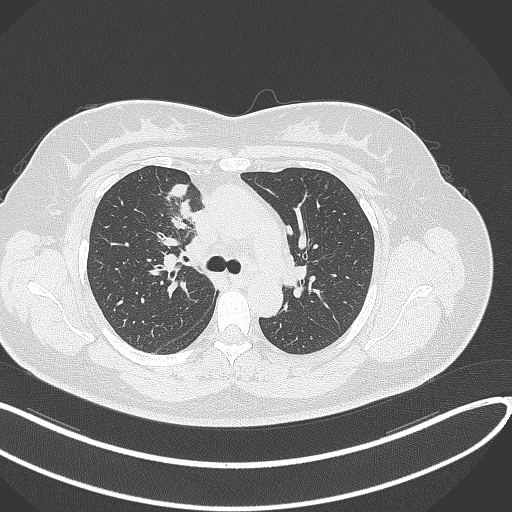
Chest CT, one axial slice; slice 188 of 303 in the series (ordered by position); reconstruction kernel B70f; 120 kVp; lung window (W 1500 / L -600 HU); 1 mm slice thickness; 512 × 512 image matrix. Female patient, age 46 years. Case-level facts recorded for this patient, not image findings: clinical TNM (as recorded): T2a N1 M0.
Outlined on this slice (rectangle marked by the reading radiologist):
- lung tumour (recorded histology: adenocarcinoma): bounding box (x1, y1, x2, y2) in pixels: (166, 182, 194, 224)